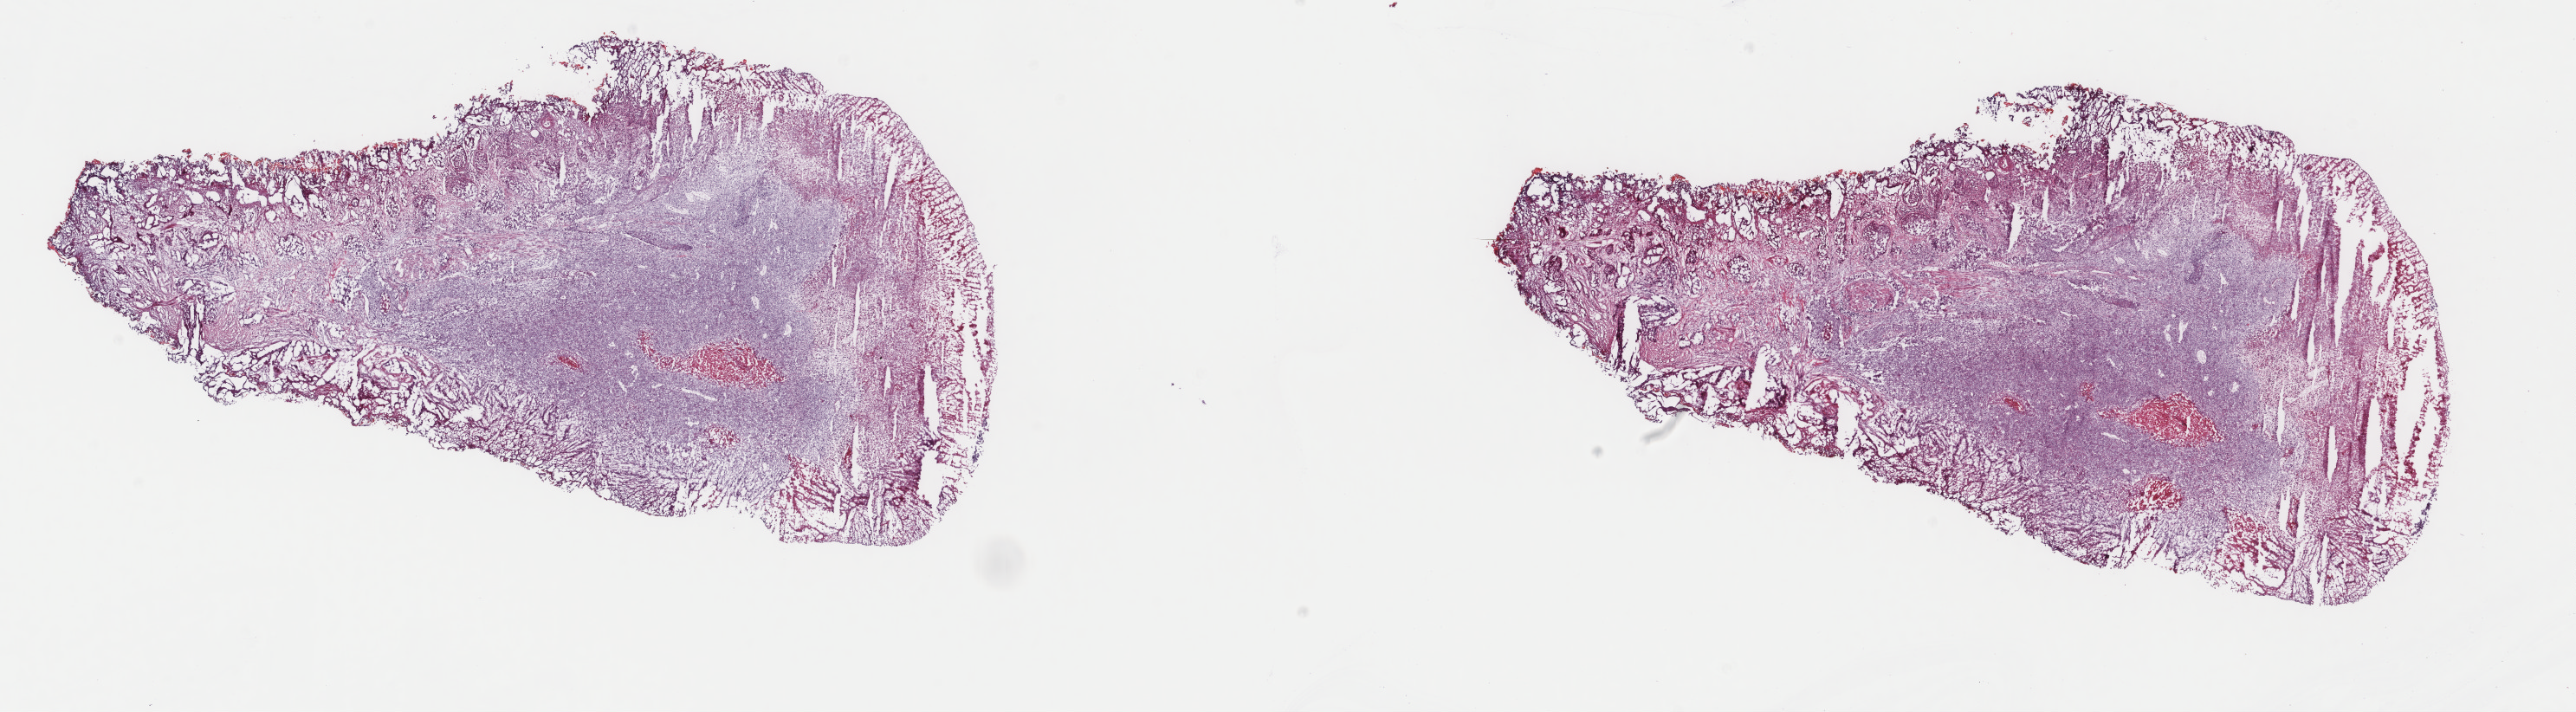
Whole-slide histology image, H&E — low-resolution overview of the scanned area, about 23.6 x 6.5 mm. Frozen section. Primary tumour sample from the bladder. Patient: female, age at initial diagnosis 54 years. Histologic grade: high grade. Pathologist review of this section (percent, as recorded): tumour cells 80%, tumour nuclei 85%, normal cells 0%, stromal cells 17%, necrosis 3%. Inflammatory infiltration, as recorded: lymphocyte infiltration 0%, monocyte infiltration 0%, neutrophil infiltration 0%.
Histologic diagnosis: Transitional cell carcinoma. AJCC pathologic stage: II (7th edition).